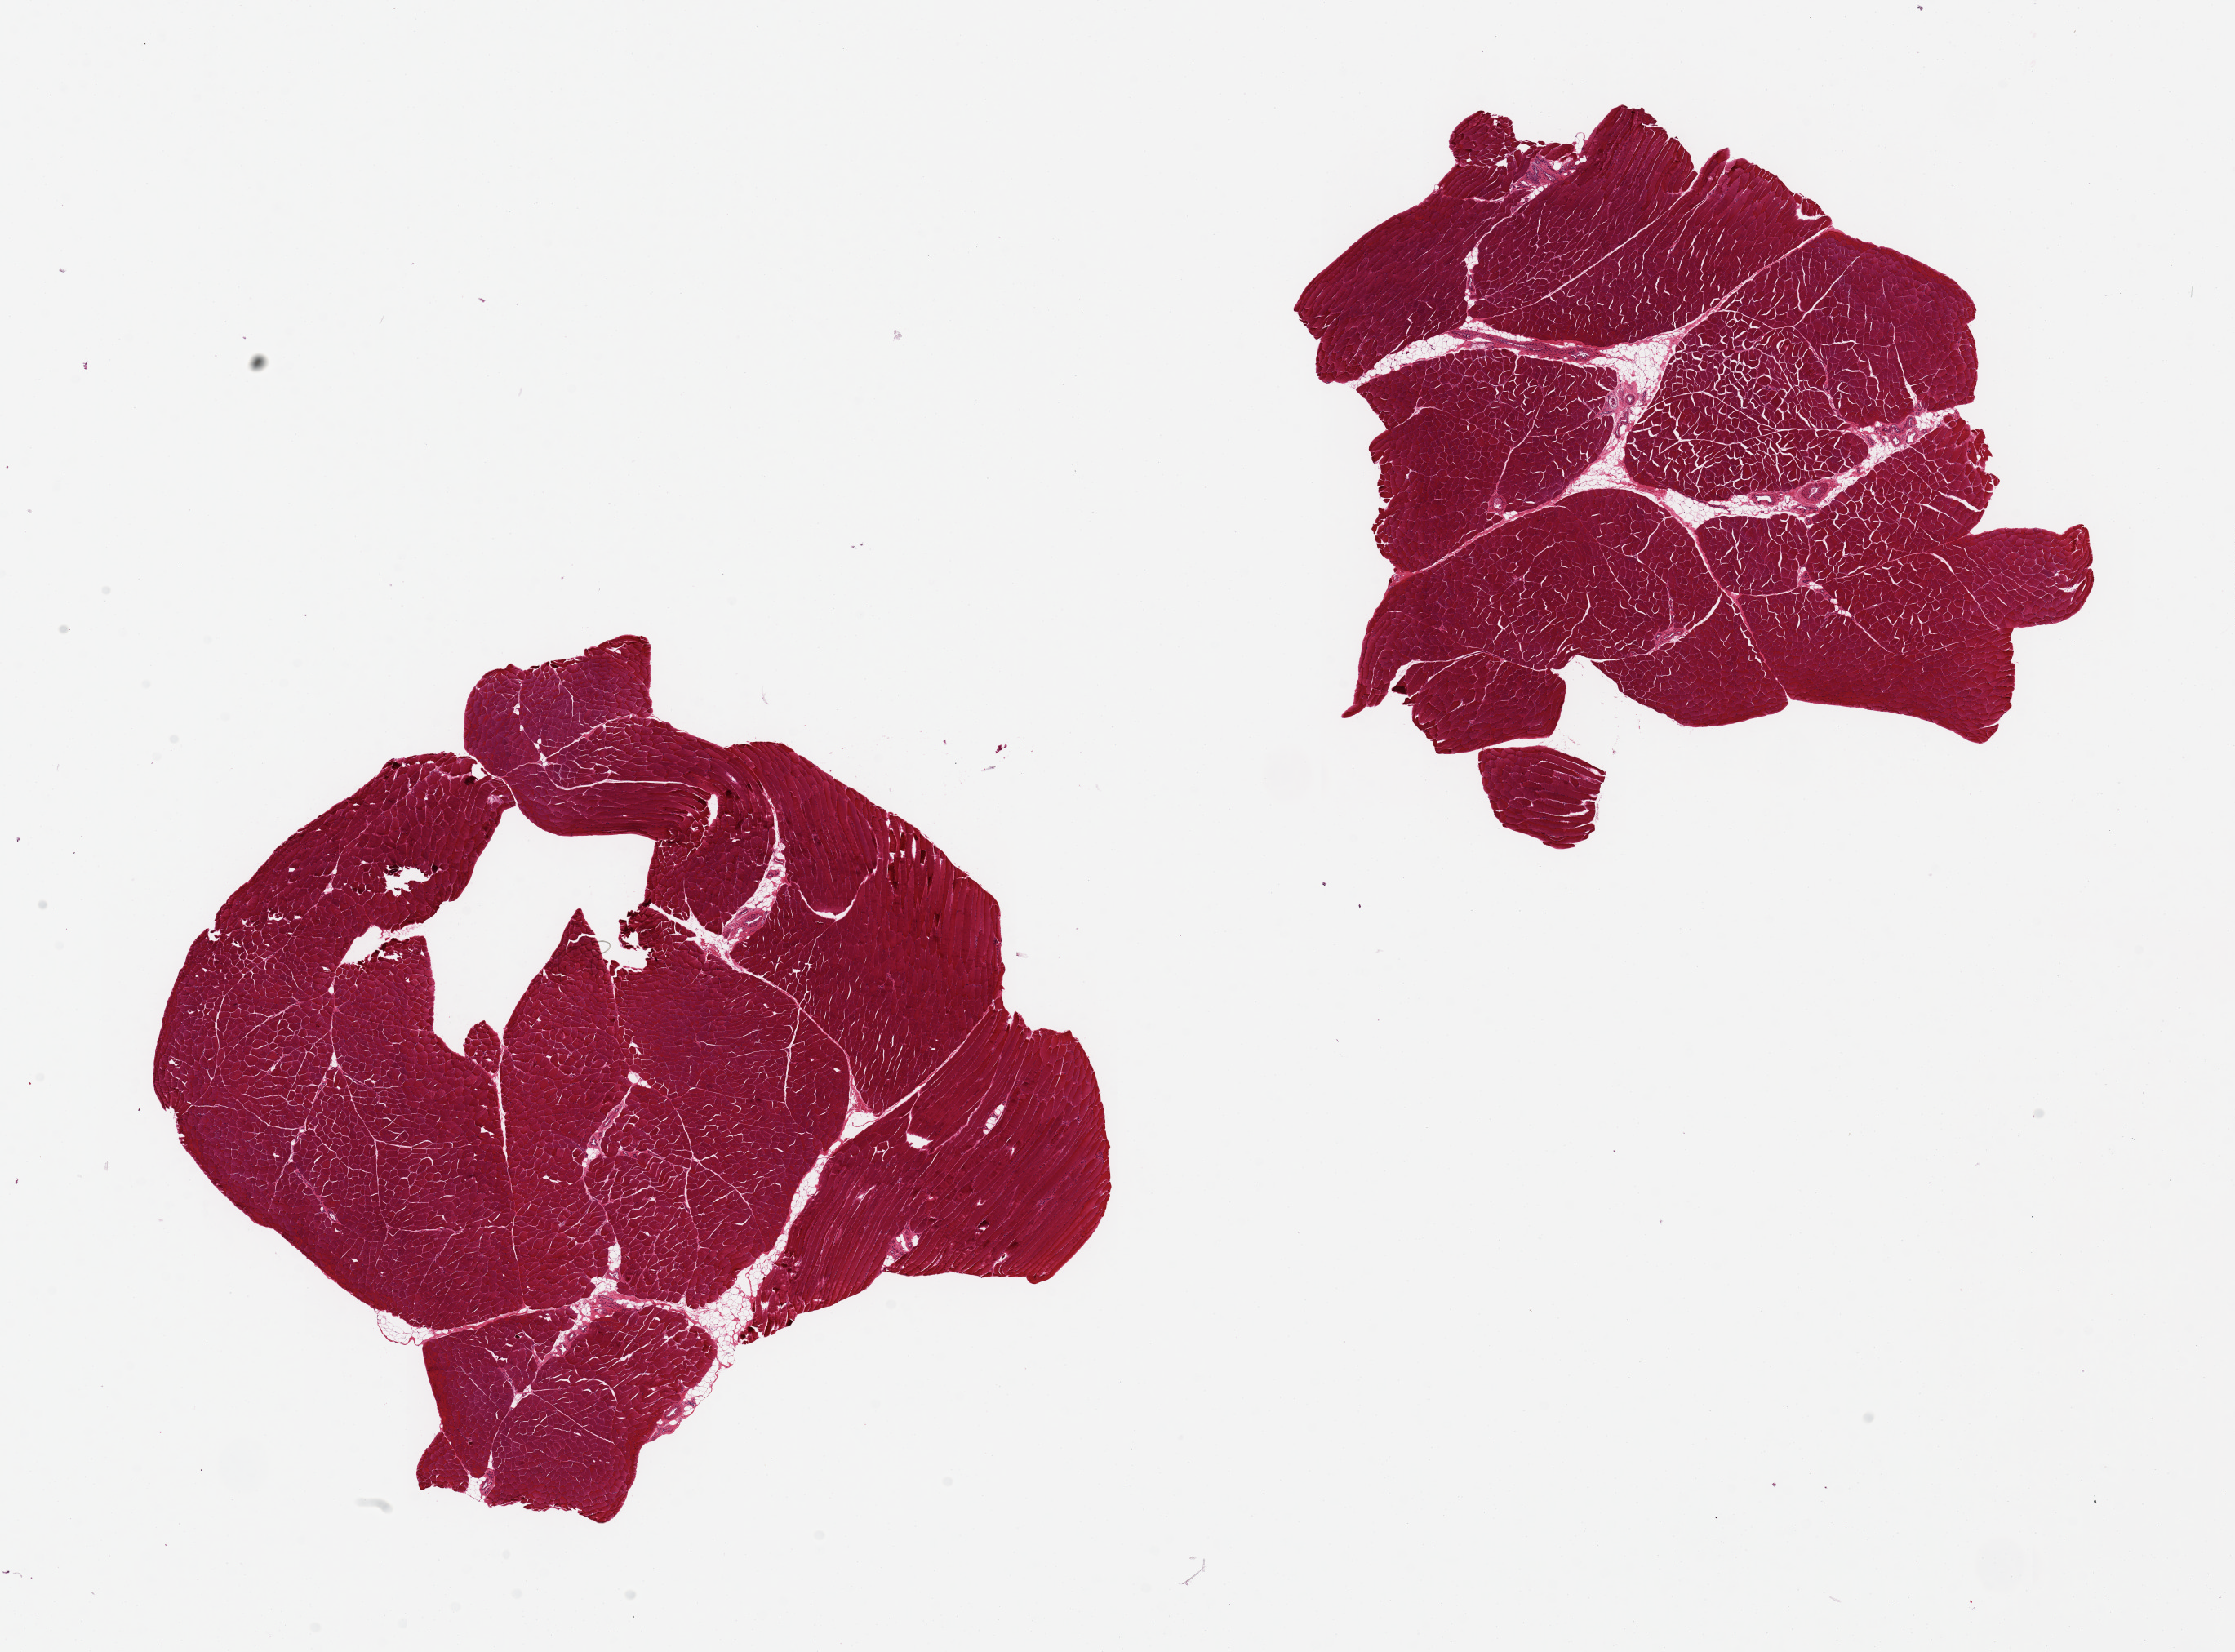
Hematoxylin and eosin (H&E) whole-slide image, brightfield — a low-resolution overview of the entire scanned area, about 21.7 x 16.0 mm; PAXgene-fixed, paraffin-embedded tissue; section of skeletal muscle (target tissue); donor tissue sample. Donor sex: male.
Review note (as recorded): 2 pieces ~7x6mm. Minimal interstitial fat.